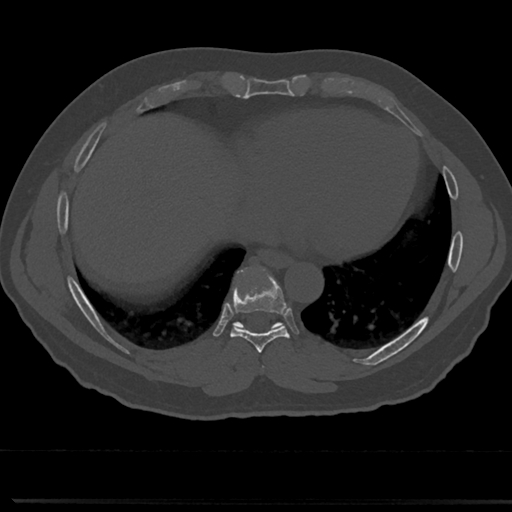
CT including the spine, one axial slice. Position 343 of 817 along the scan axis. Reconstruction kernel Br40s/3. Bone window (W 1800 / L 400 HU). 512 × 512 image matrix. Male patient, age 61 years. From the clinical record (not read from this slice): primary cancer: prostate.
Outlined on this slice (semi-automatic segmentation, software-assisted and operator-edited):
- T7 vertebra: box from (x=256, y=342) to (x=268, y=377) px
- T8 vertebra: (x=214, y=271)–(x=306, y=354)